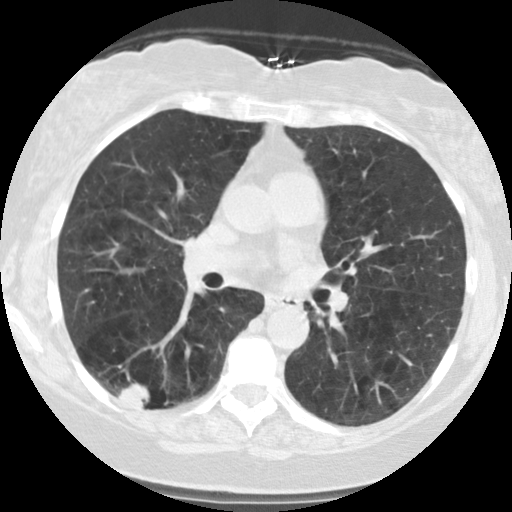
Low-dose screening chest CT, one axial slice. Slice 63 of 122 in the series (ordered by position). Reconstruction kernel STANDARD. 140 kVp. Lung window (W 1500 / L -600 HU). 2.5 mm slice thickness. 512 × 512 image matrix.
Structures marked on this image (manually delineated by an expert):
- lesion 1 (tumor, lower lobe of right lung): box from (x=118, y=383) to (x=150, y=408) px